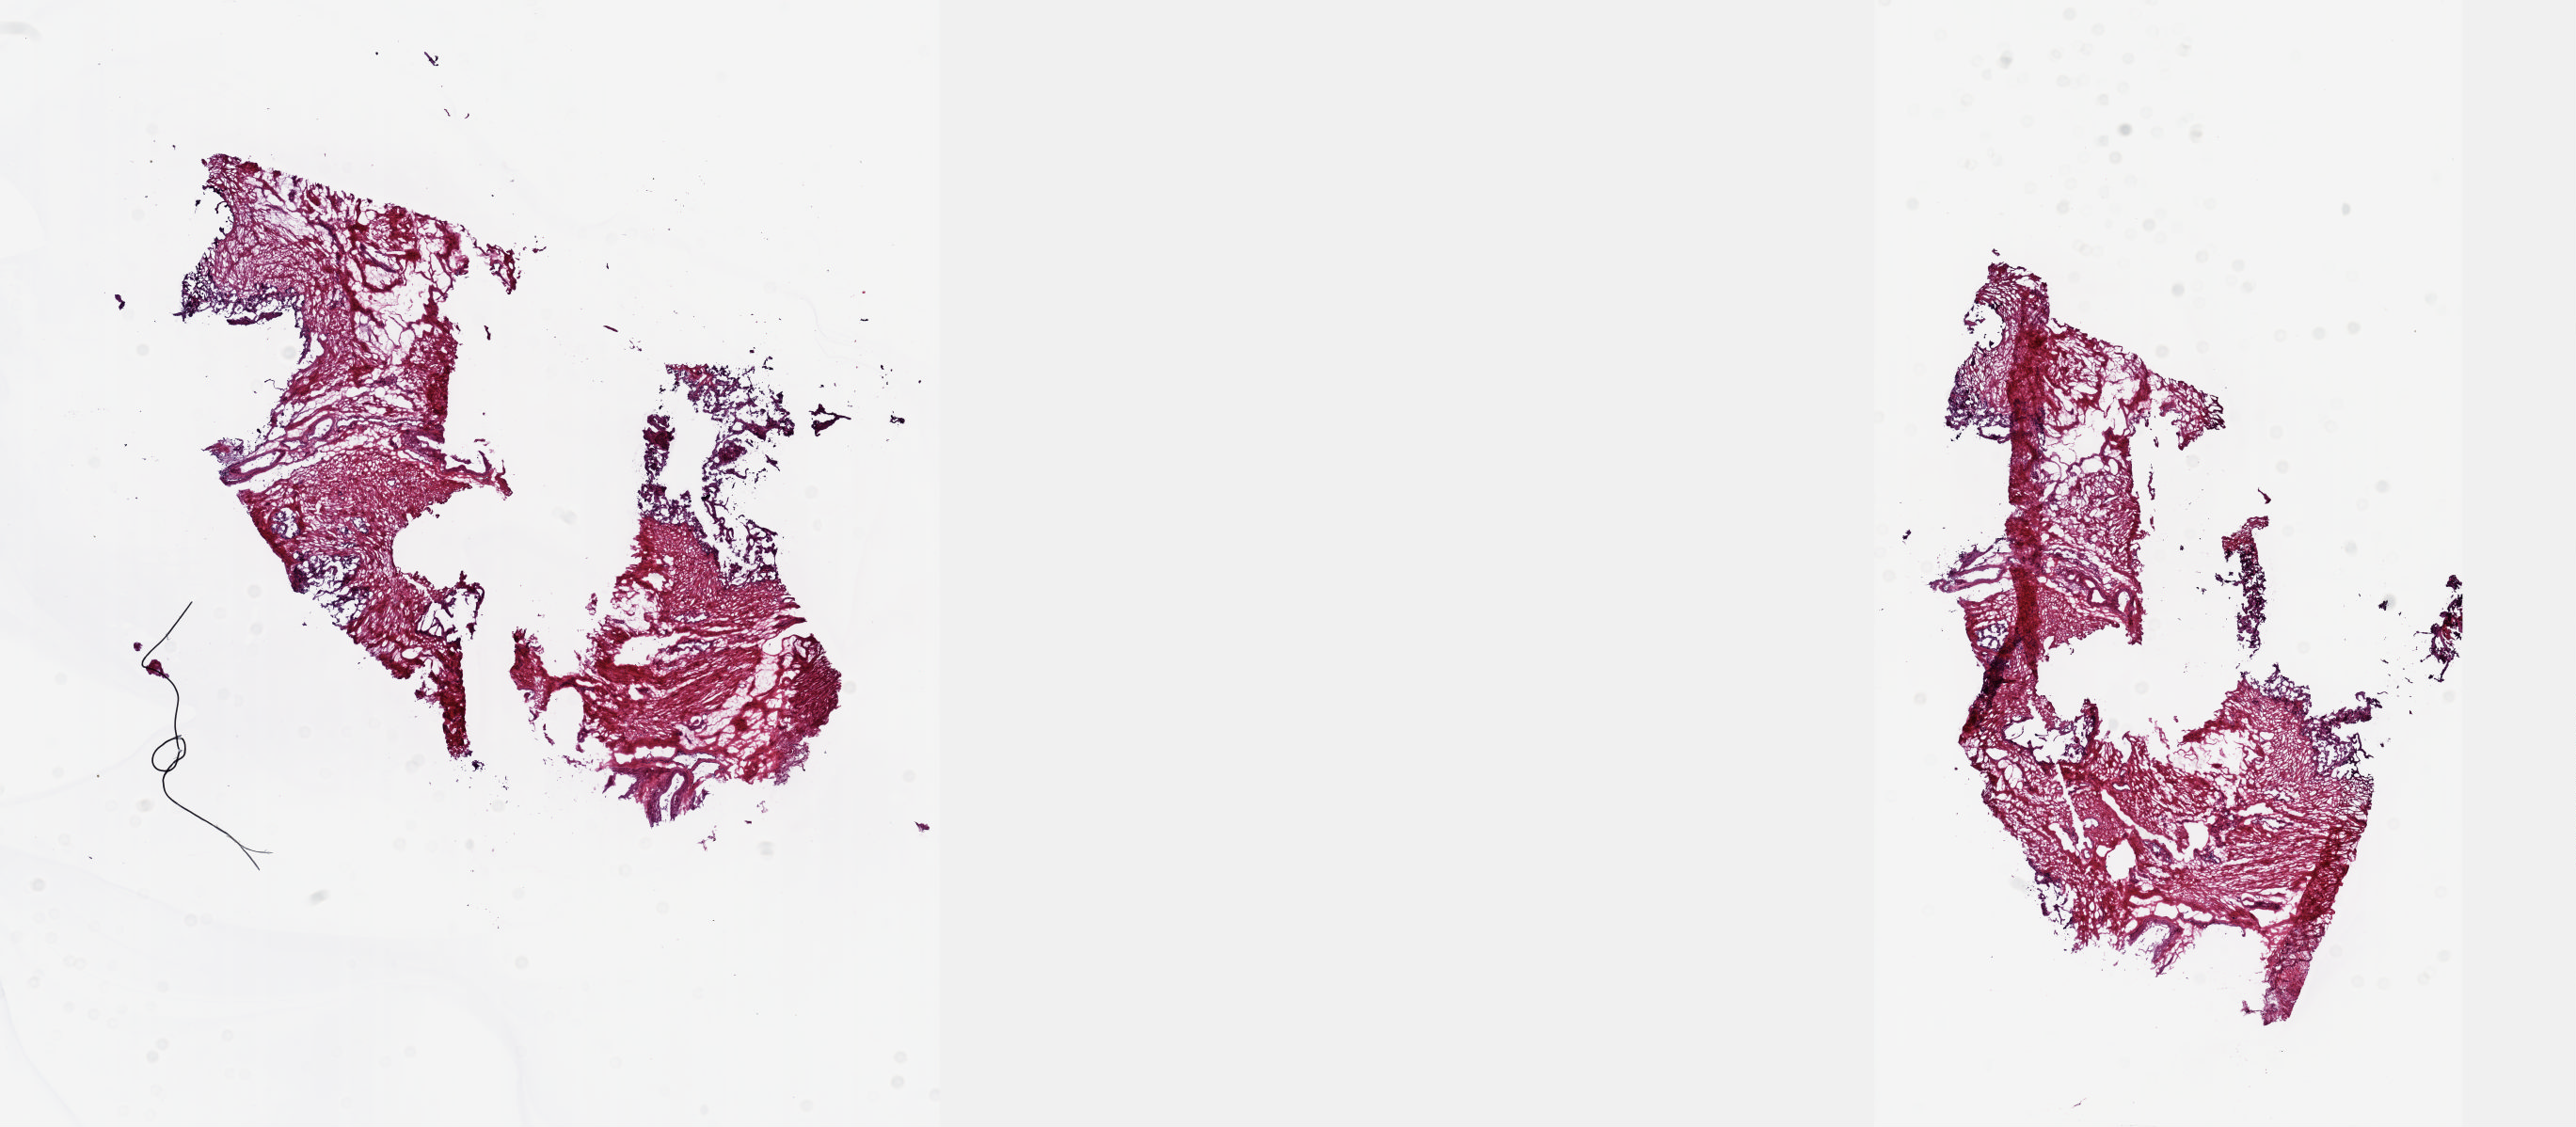
Whole-slide histology image, H&E, a low-resolution overview of the entire scanned area, about 22.1 x 9.7 mm (acquisition: 20x scan). Frozen section from the top of the tissue portion. Prostate, solid tissue normal (non-tumour tissue) sample. Patient: male, age at initial diagnosis 56 years. Pathologist review of this section (percent, as recorded): tumour cells 0%, tumour nuclei 0%, normal cells 18%, stromal cells 82%, necrosis 0%. Inflammatory infiltration, as recorded: lymphocyte infiltration 3%, monocyte infiltration 0%, neutrophil infiltration 0%.
This section: solid tissue normal sample (biorepository sample class). Patient diagnosis: Adenocarcinoma, NOS (prostate gland).